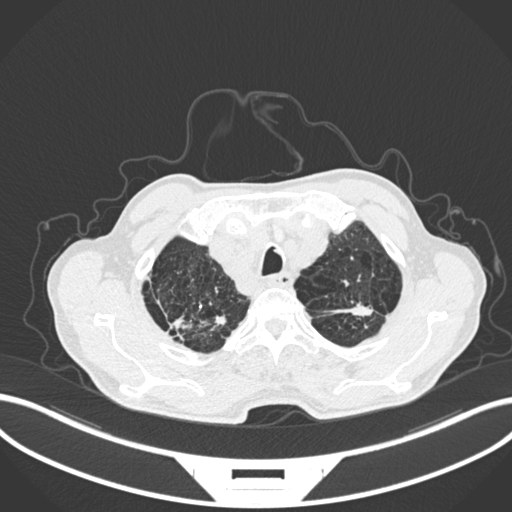
Chest CT, one axial slice. Position 242 of 287 along the scan axis. 120 kVp. Lung window (W 1500 / L -600 HU). 1 mm slice thickness. 512 × 512 image matrix, field of view 400 × 400 mm. Patient: male, 74 years. From the clinical record (not read from this slice): clinical TNM (as recorded): T2a N1 M0.
Structures marked on this image (bounding box drawn by a radiologist):
- lung tumour (recorded histology: adenocarcinoma): bounding box <338,300,383,318> (left, top, right, bottom; pixels)